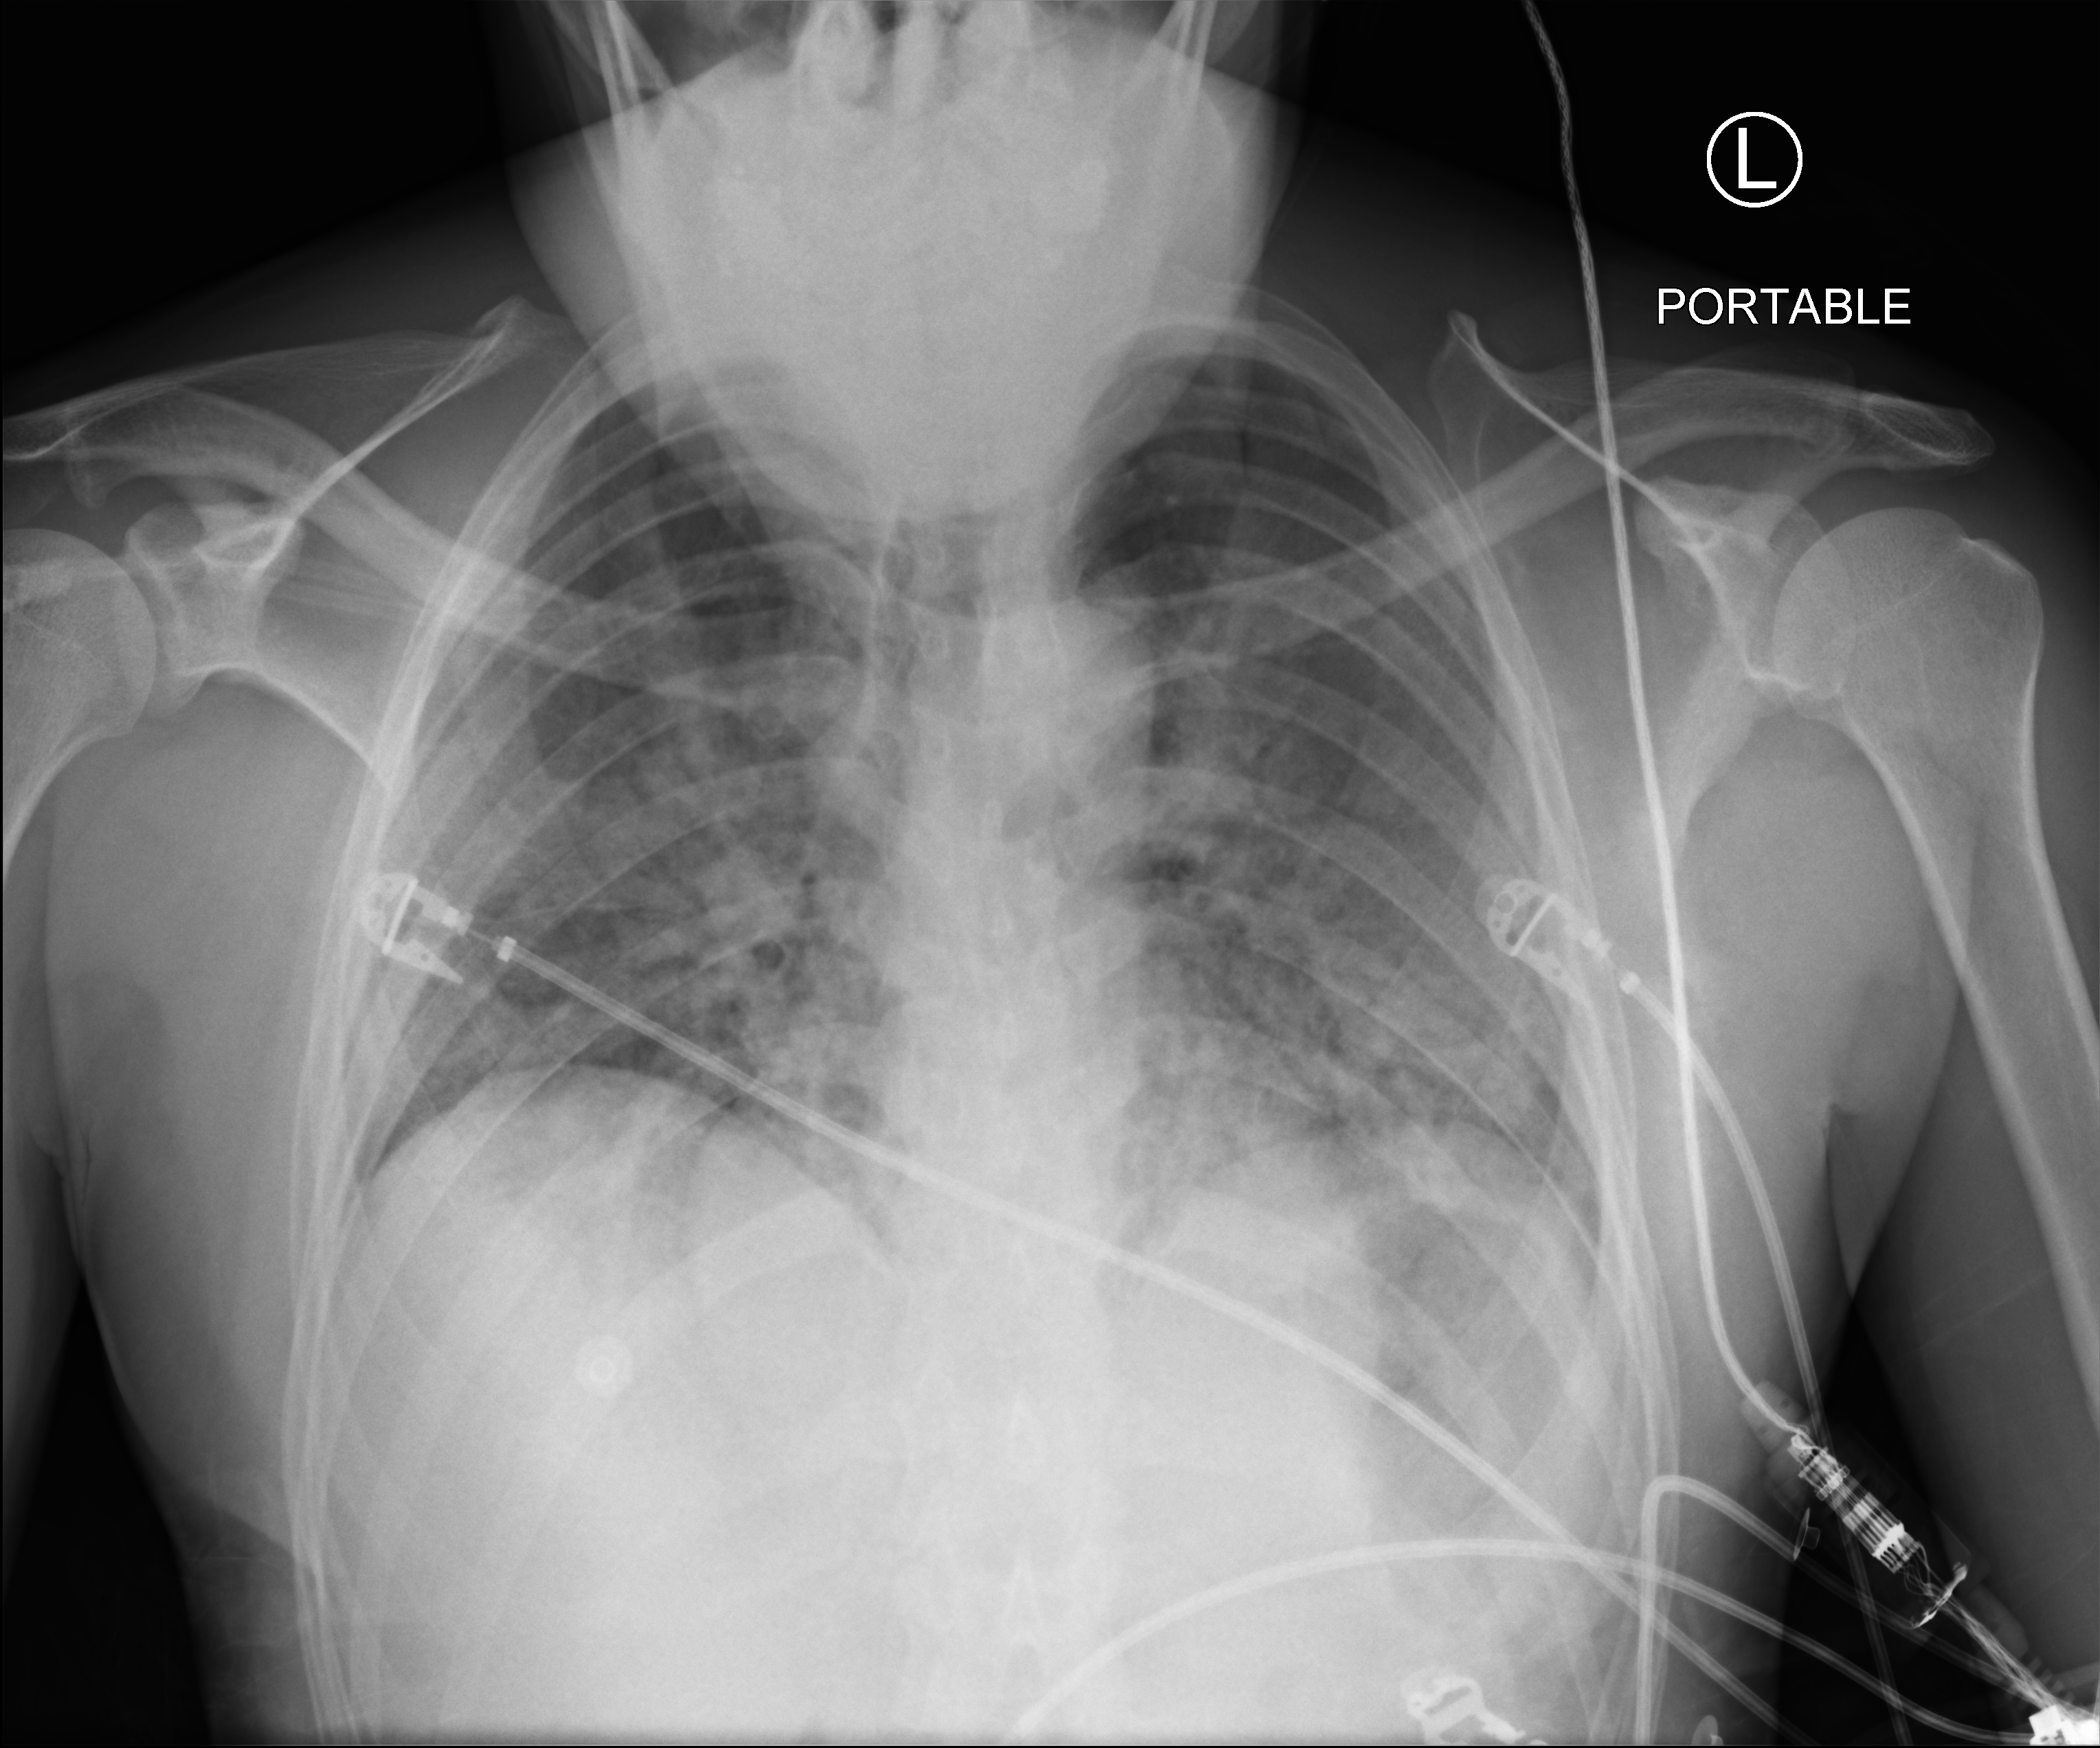
Bedside chest radiograph (computed radiography); anteroposterior (AP) projection. Male patient hospitalised with COVID-19, age 18–59 years.
Admission-level facts for this patient (not findings on this image; timing relative to this image not recorded): length of hospital stay: 14 days; admitted to intensive care during this hospital stay: yes; other chronic lung disease (admission record): no.